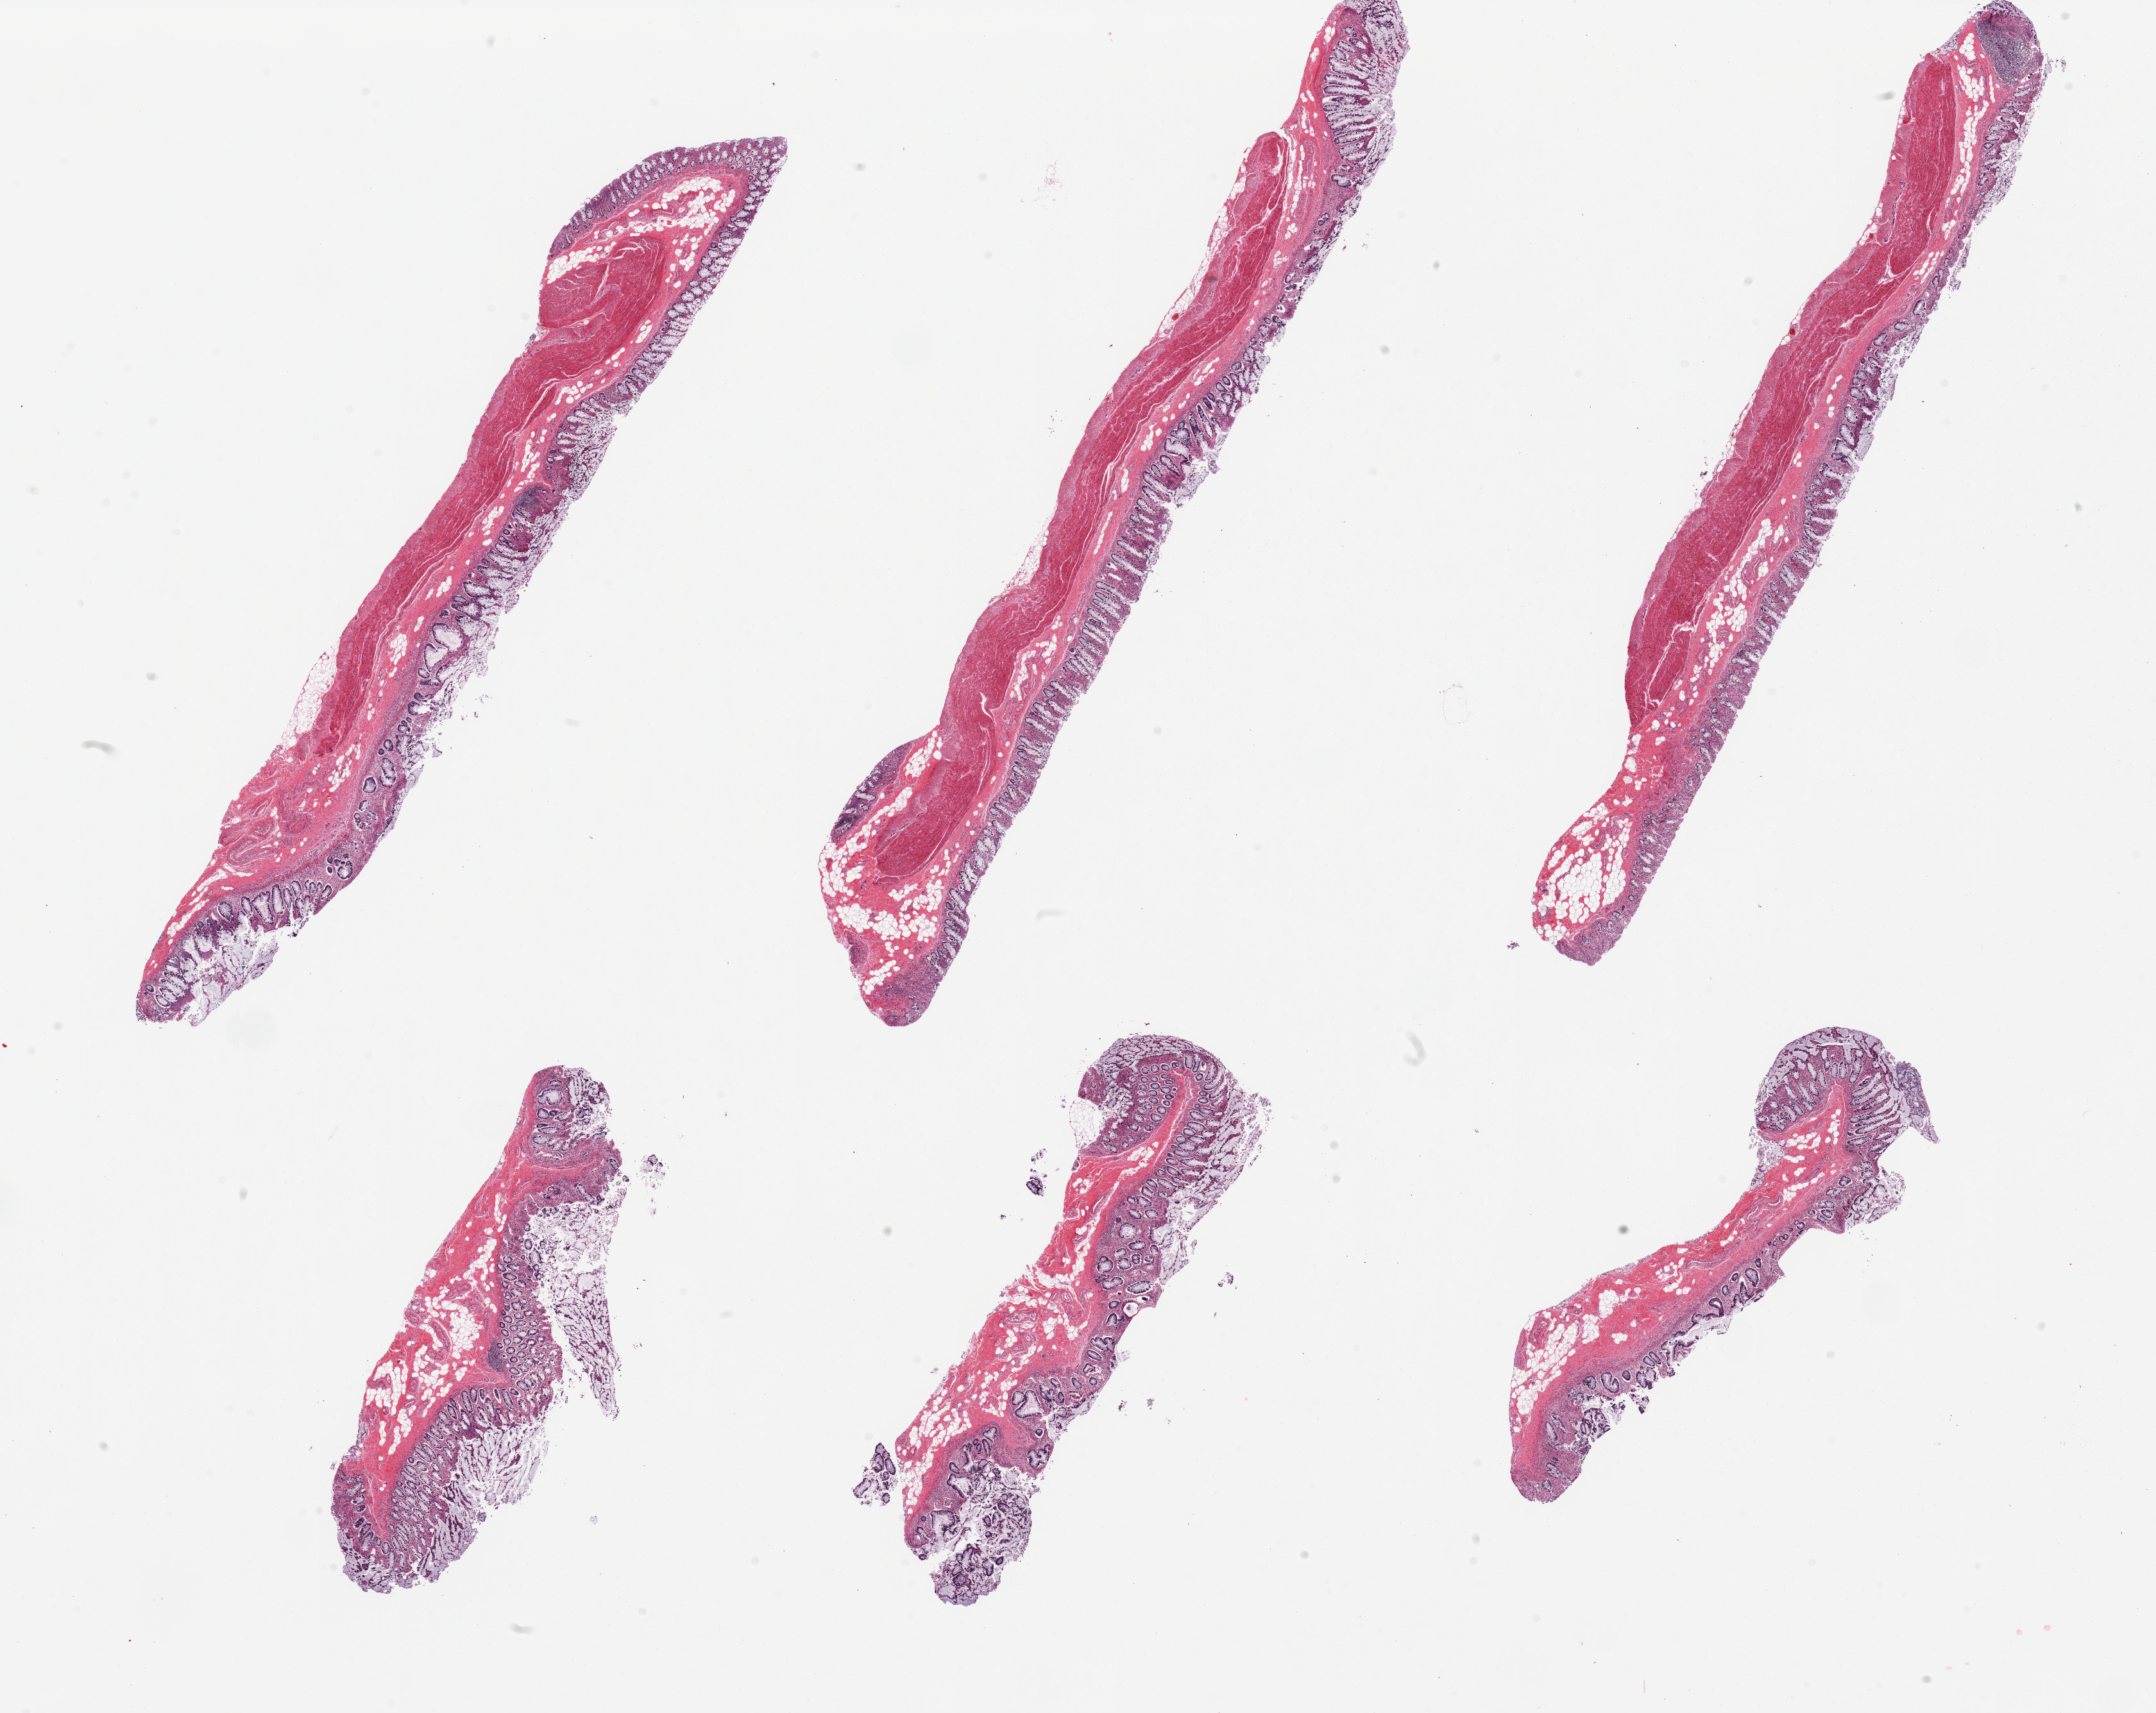
Whole-slide image, haematoxylin and eosin stain — whole scanned area (about 26.6 x 21.1 mm, from a 20x scan) shown as a low-resolution overview. PAXgene-fixed, paraffin-embedded tissue. Sampled site (target tissue): transverse colon. Tissue donor sample.
Review note (as recorded): 6 pieces; moderately autolyzed mucosa in all; 3 have no muscularis.